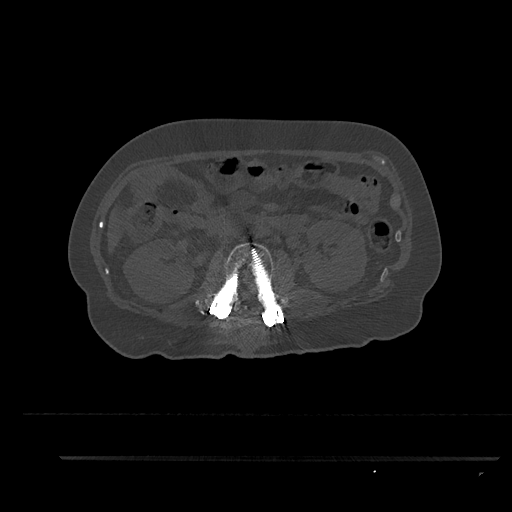
CT including the spine, one axial slice; position 165 of 797 along the scan axis; bone window (W 1800 / L 400 HU); 0.5 mm slice thickness; 512 × 512 image matrix. Female patient, age 44 years. Case-level facts recorded for this patient, not image findings: primary cancer: renal; vertebrae with lytic lesions (as recorded): L1.
Annotated regions visible in this slice (semi-automatically segmented with operator editing):
- L2 vertebra: bounding box <195,242,286,320> (left, top, right, bottom; pixels)